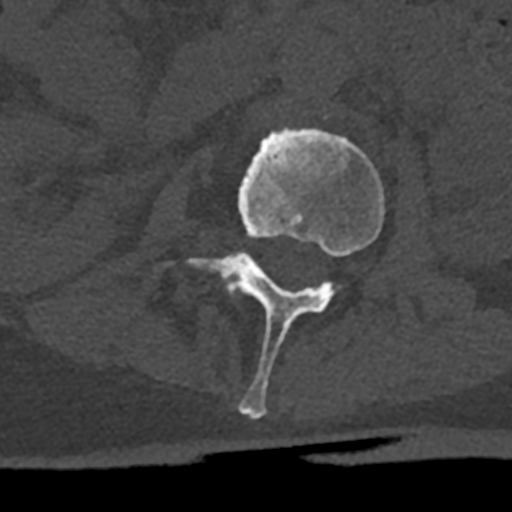
CT including the spine, one axial slice. Position 370 of 797 along the scan axis. Reconstruction kernel Br40s/3. Bone window (W 1800 / L 400 HU). 0.5 mm slice thickness. 512 × 512 image matrix, field of view 160 × 160 mm. Male patient, age 74 years. From the clinical record (not read from this slice): primary cancer: renal; vertebrae with lytic lesions (as recorded): T10, L1, L2, L3, L4, L5.
Annotated regions visible in this slice (semi-automatically segmented with operator editing):
- L2 vertebra: bounding box [x1, y1, x2, y2] px = [180, 128, 384, 419]
- L3 vertebra: [227, 252, 245, 293]